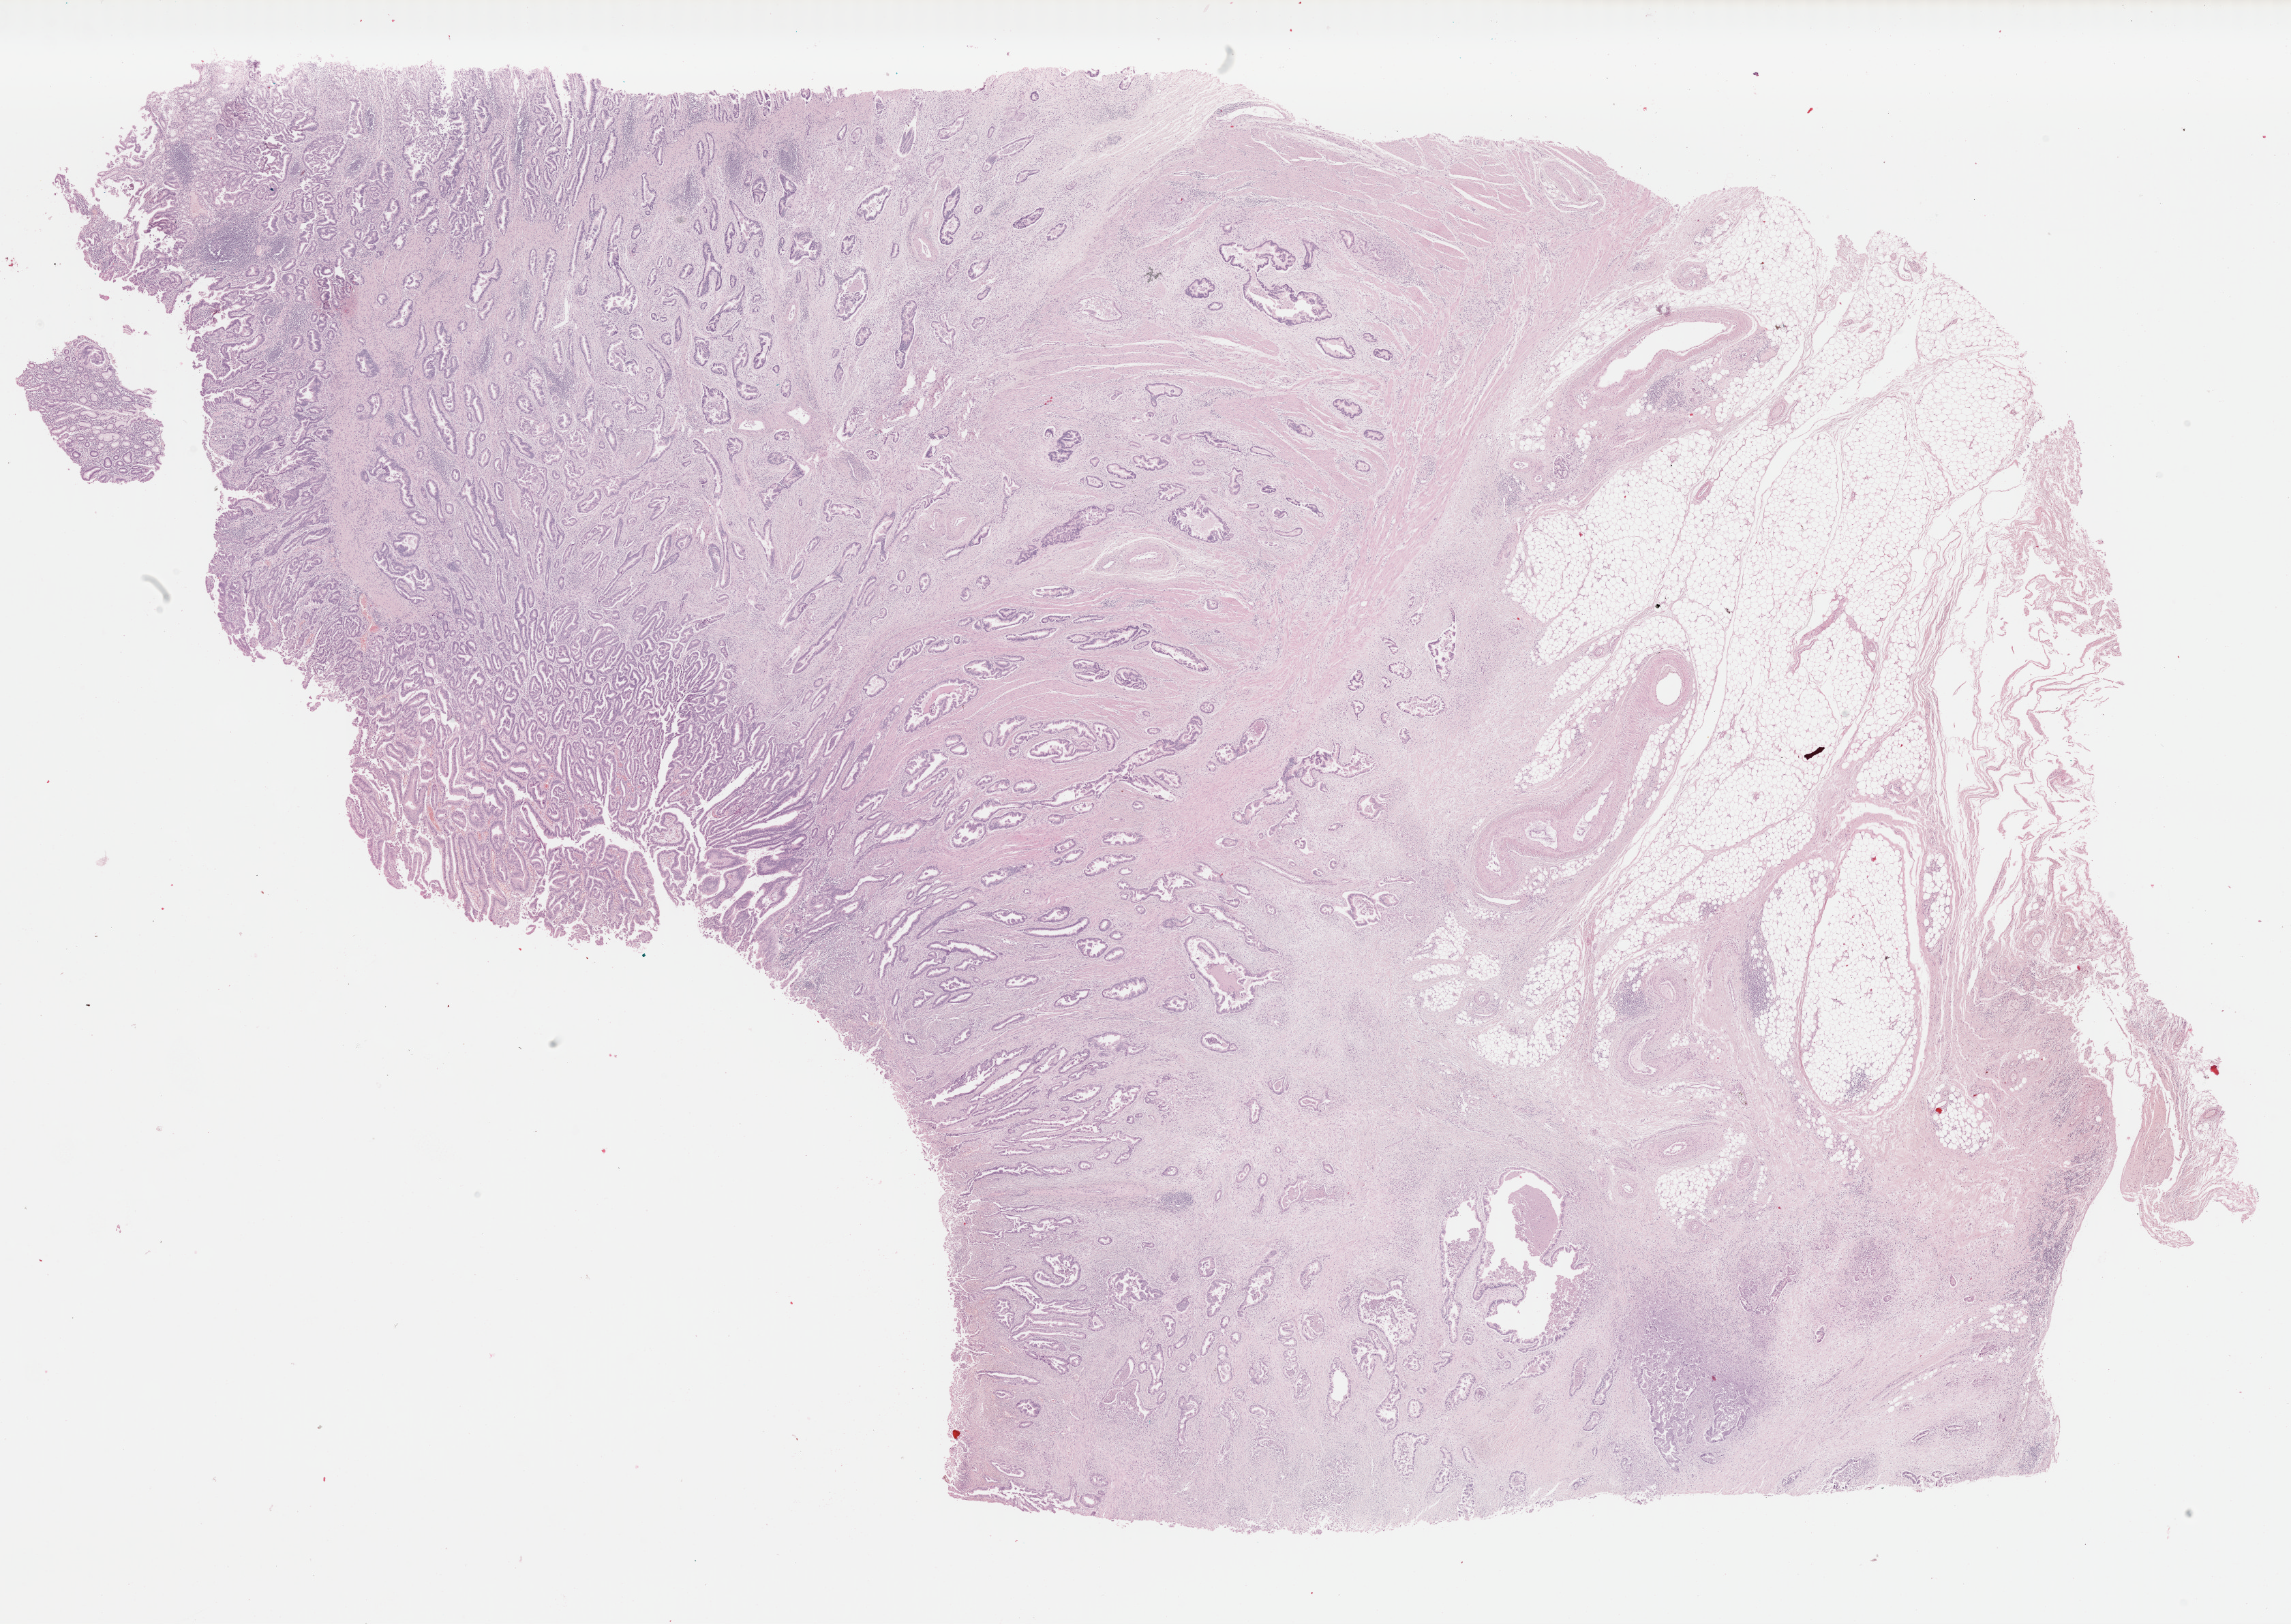
Whole-slide histology image, H&E-stained, whole scanned area (about 26.4 x 18.7 mm, slide scanned at 40x) shown as a low-resolution overview, formalin-fixed paraffin-embedded (FFPE) diagnostic section, primary tumour sample from the stomach. Male patient; age at initial diagnosis 63 years.
Diagnosis: Tubular adenocarcinoma (body of stomach).